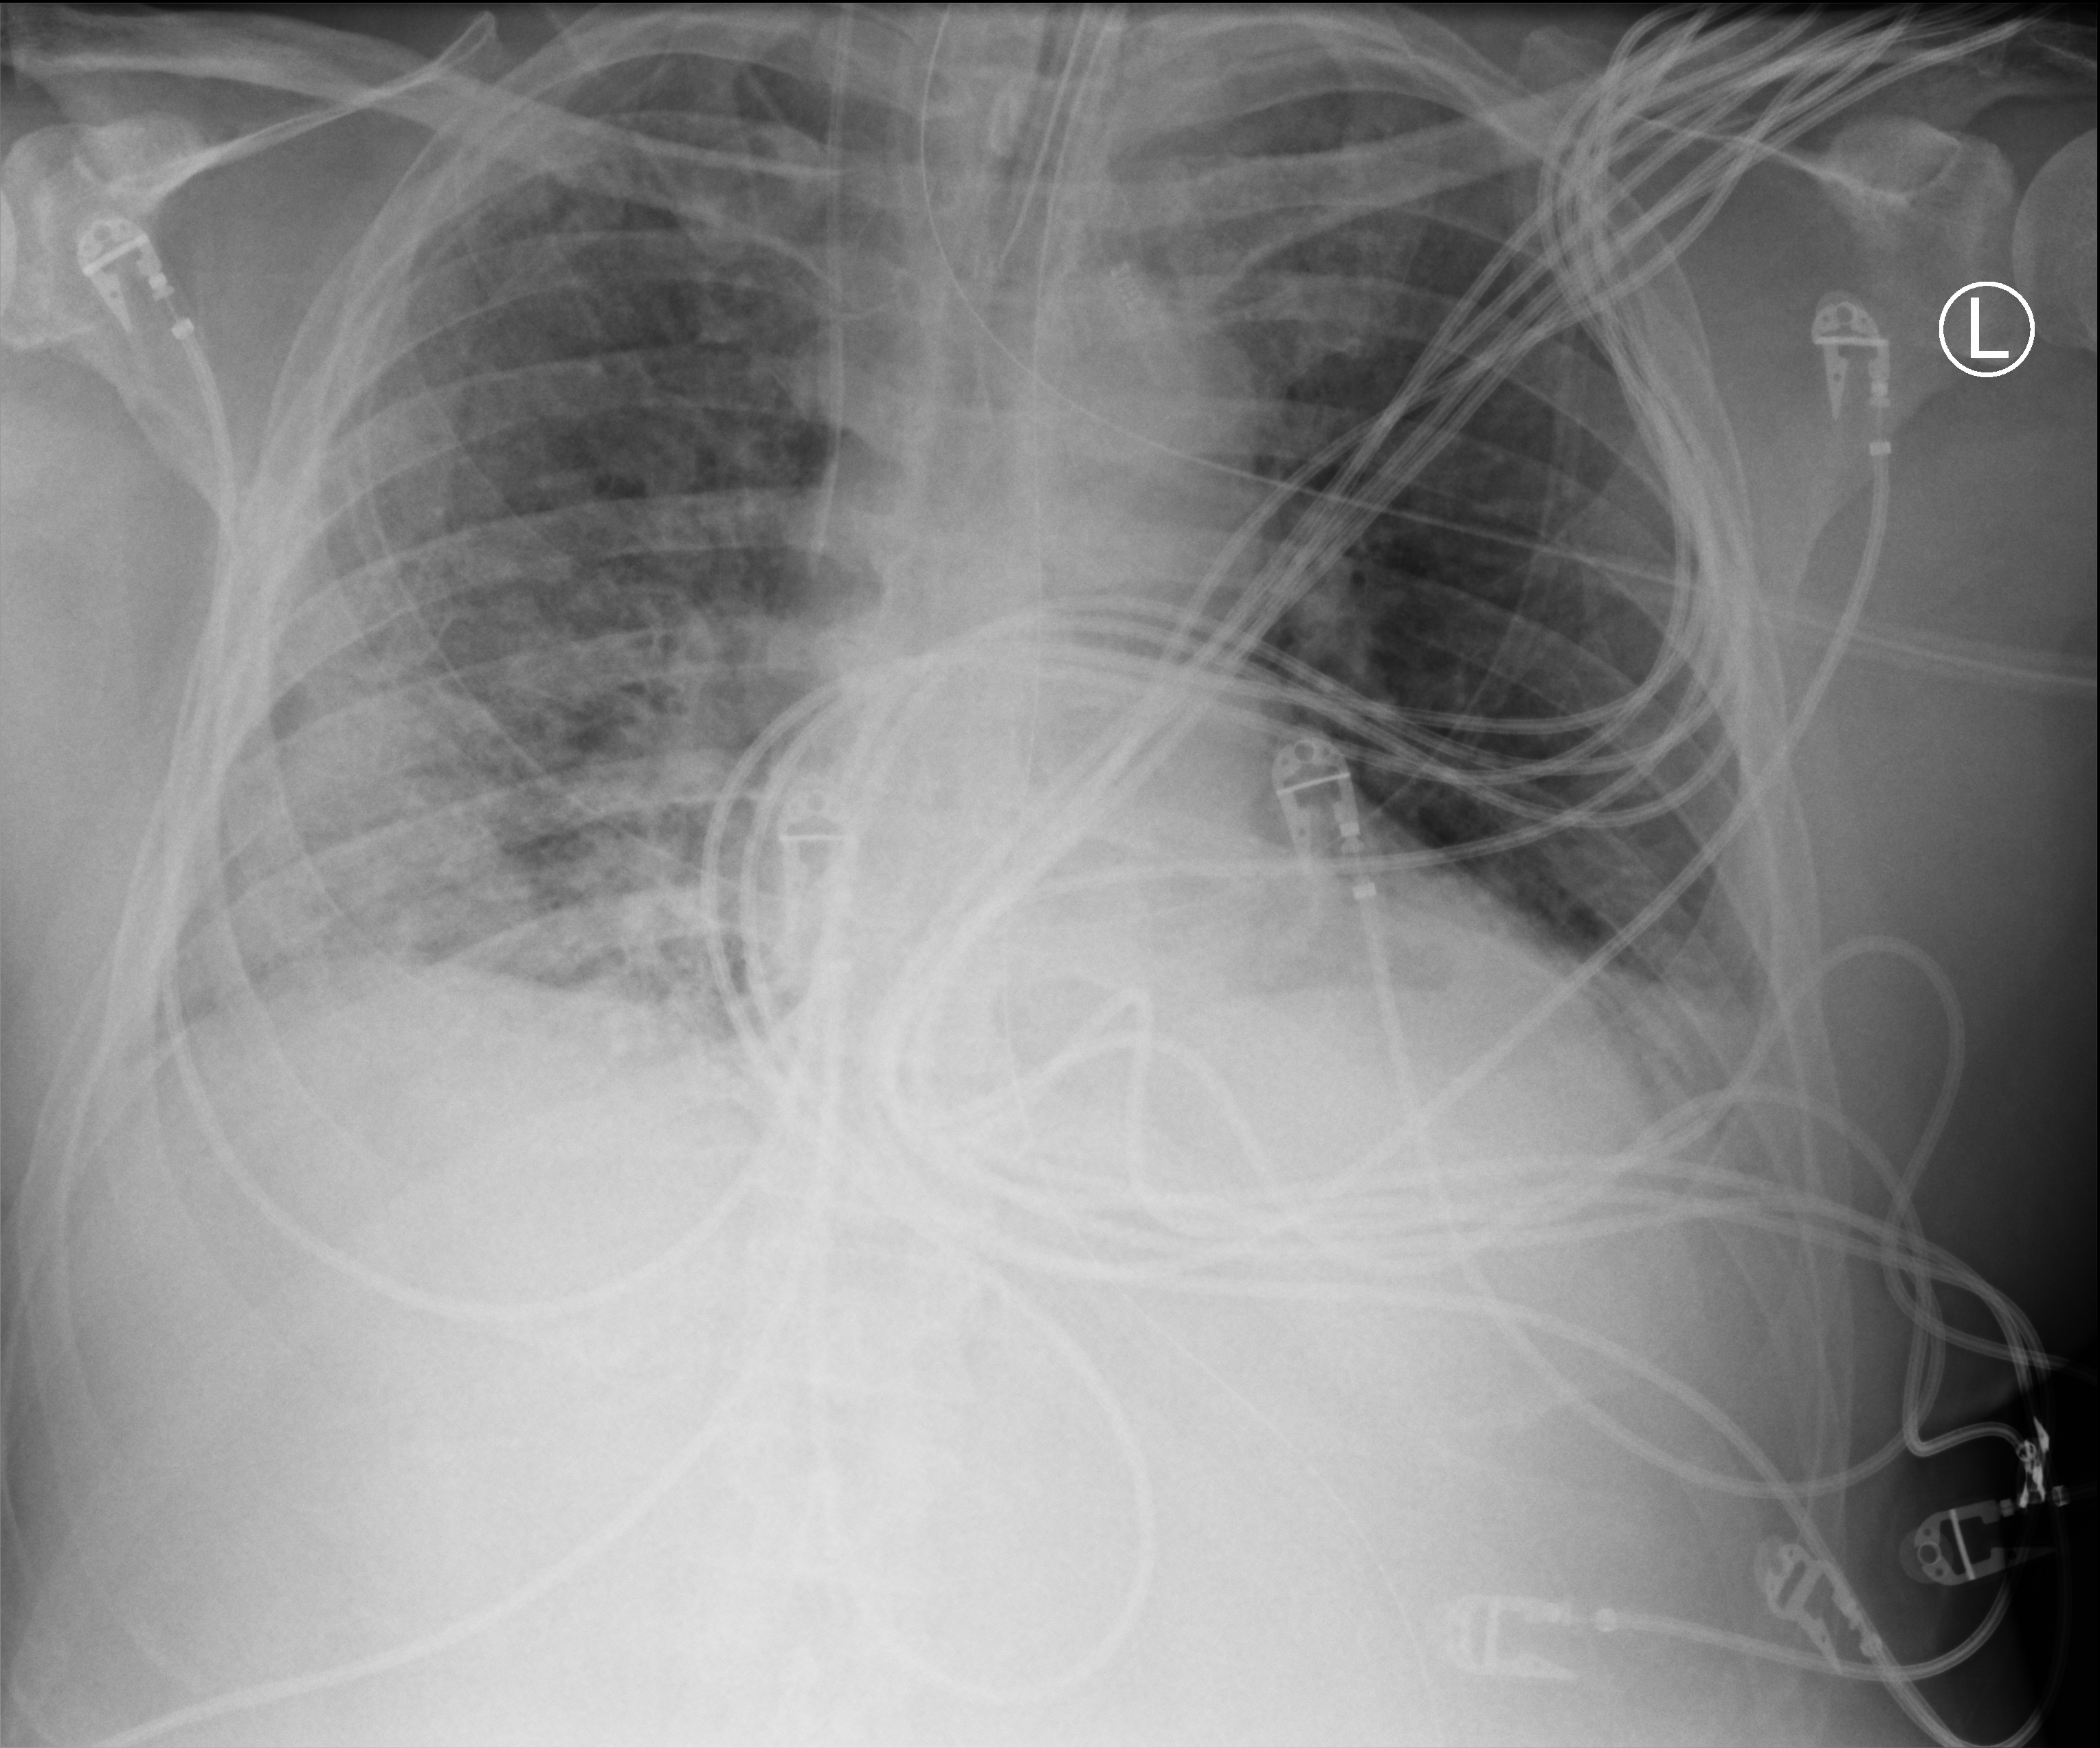
Chest X-ray (portable), anteroposterior (AP) projection. Patient hospitalised with COVID-19; male, aged 60–74 years.
From the hospital-stay record, not from the radiograph (when in the stay this image was taken is not recorded): other chronic lung disease (admission record): no; diabetes (admission record): no.